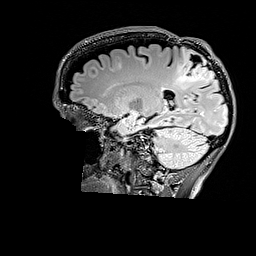
Brain MRI from a brain-tumour surgery series, one sagittal slice; slice 110 of 176 in the series (ordered by position); T2 FLAIR; 1 mm slice thickness; 256 × 256 image matrix, field of view 256 × 256 mm. From the clinical record (not read from this slice): histopathology: Astrocytoma; WHO grade: 3; IDH mutation: yes.
Outlined on this slice (manually delineated by an expert):
- tumour: box from (x=175, y=49) to (x=216, y=87) px
- tumour: (x=185, y=59)–(x=214, y=83)